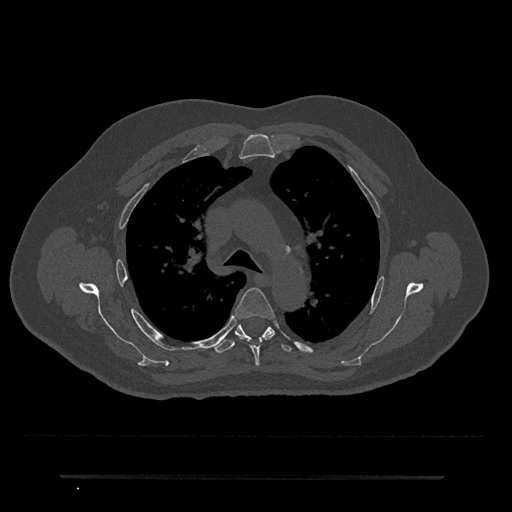
CT including the spine, one axial slice; slice 509 of 797 in the series (ordered by position); reconstruction kernel Br40s/3; bone window (W 1800 / L 400 HU); 0.5 mm slice thickness; 512 × 512 image matrix. Patient: male, 69 years. From the clinical record (not read from this slice): primary cancer: prostate.
Outlined on this slice (semi-automatic segmentation, software-assisted and operator-edited):
- T4 vertebra: box from (x=234, y=288) to (x=275, y=366) px
- T5 vertebra: (x=213, y=324)–(x=292, y=353)